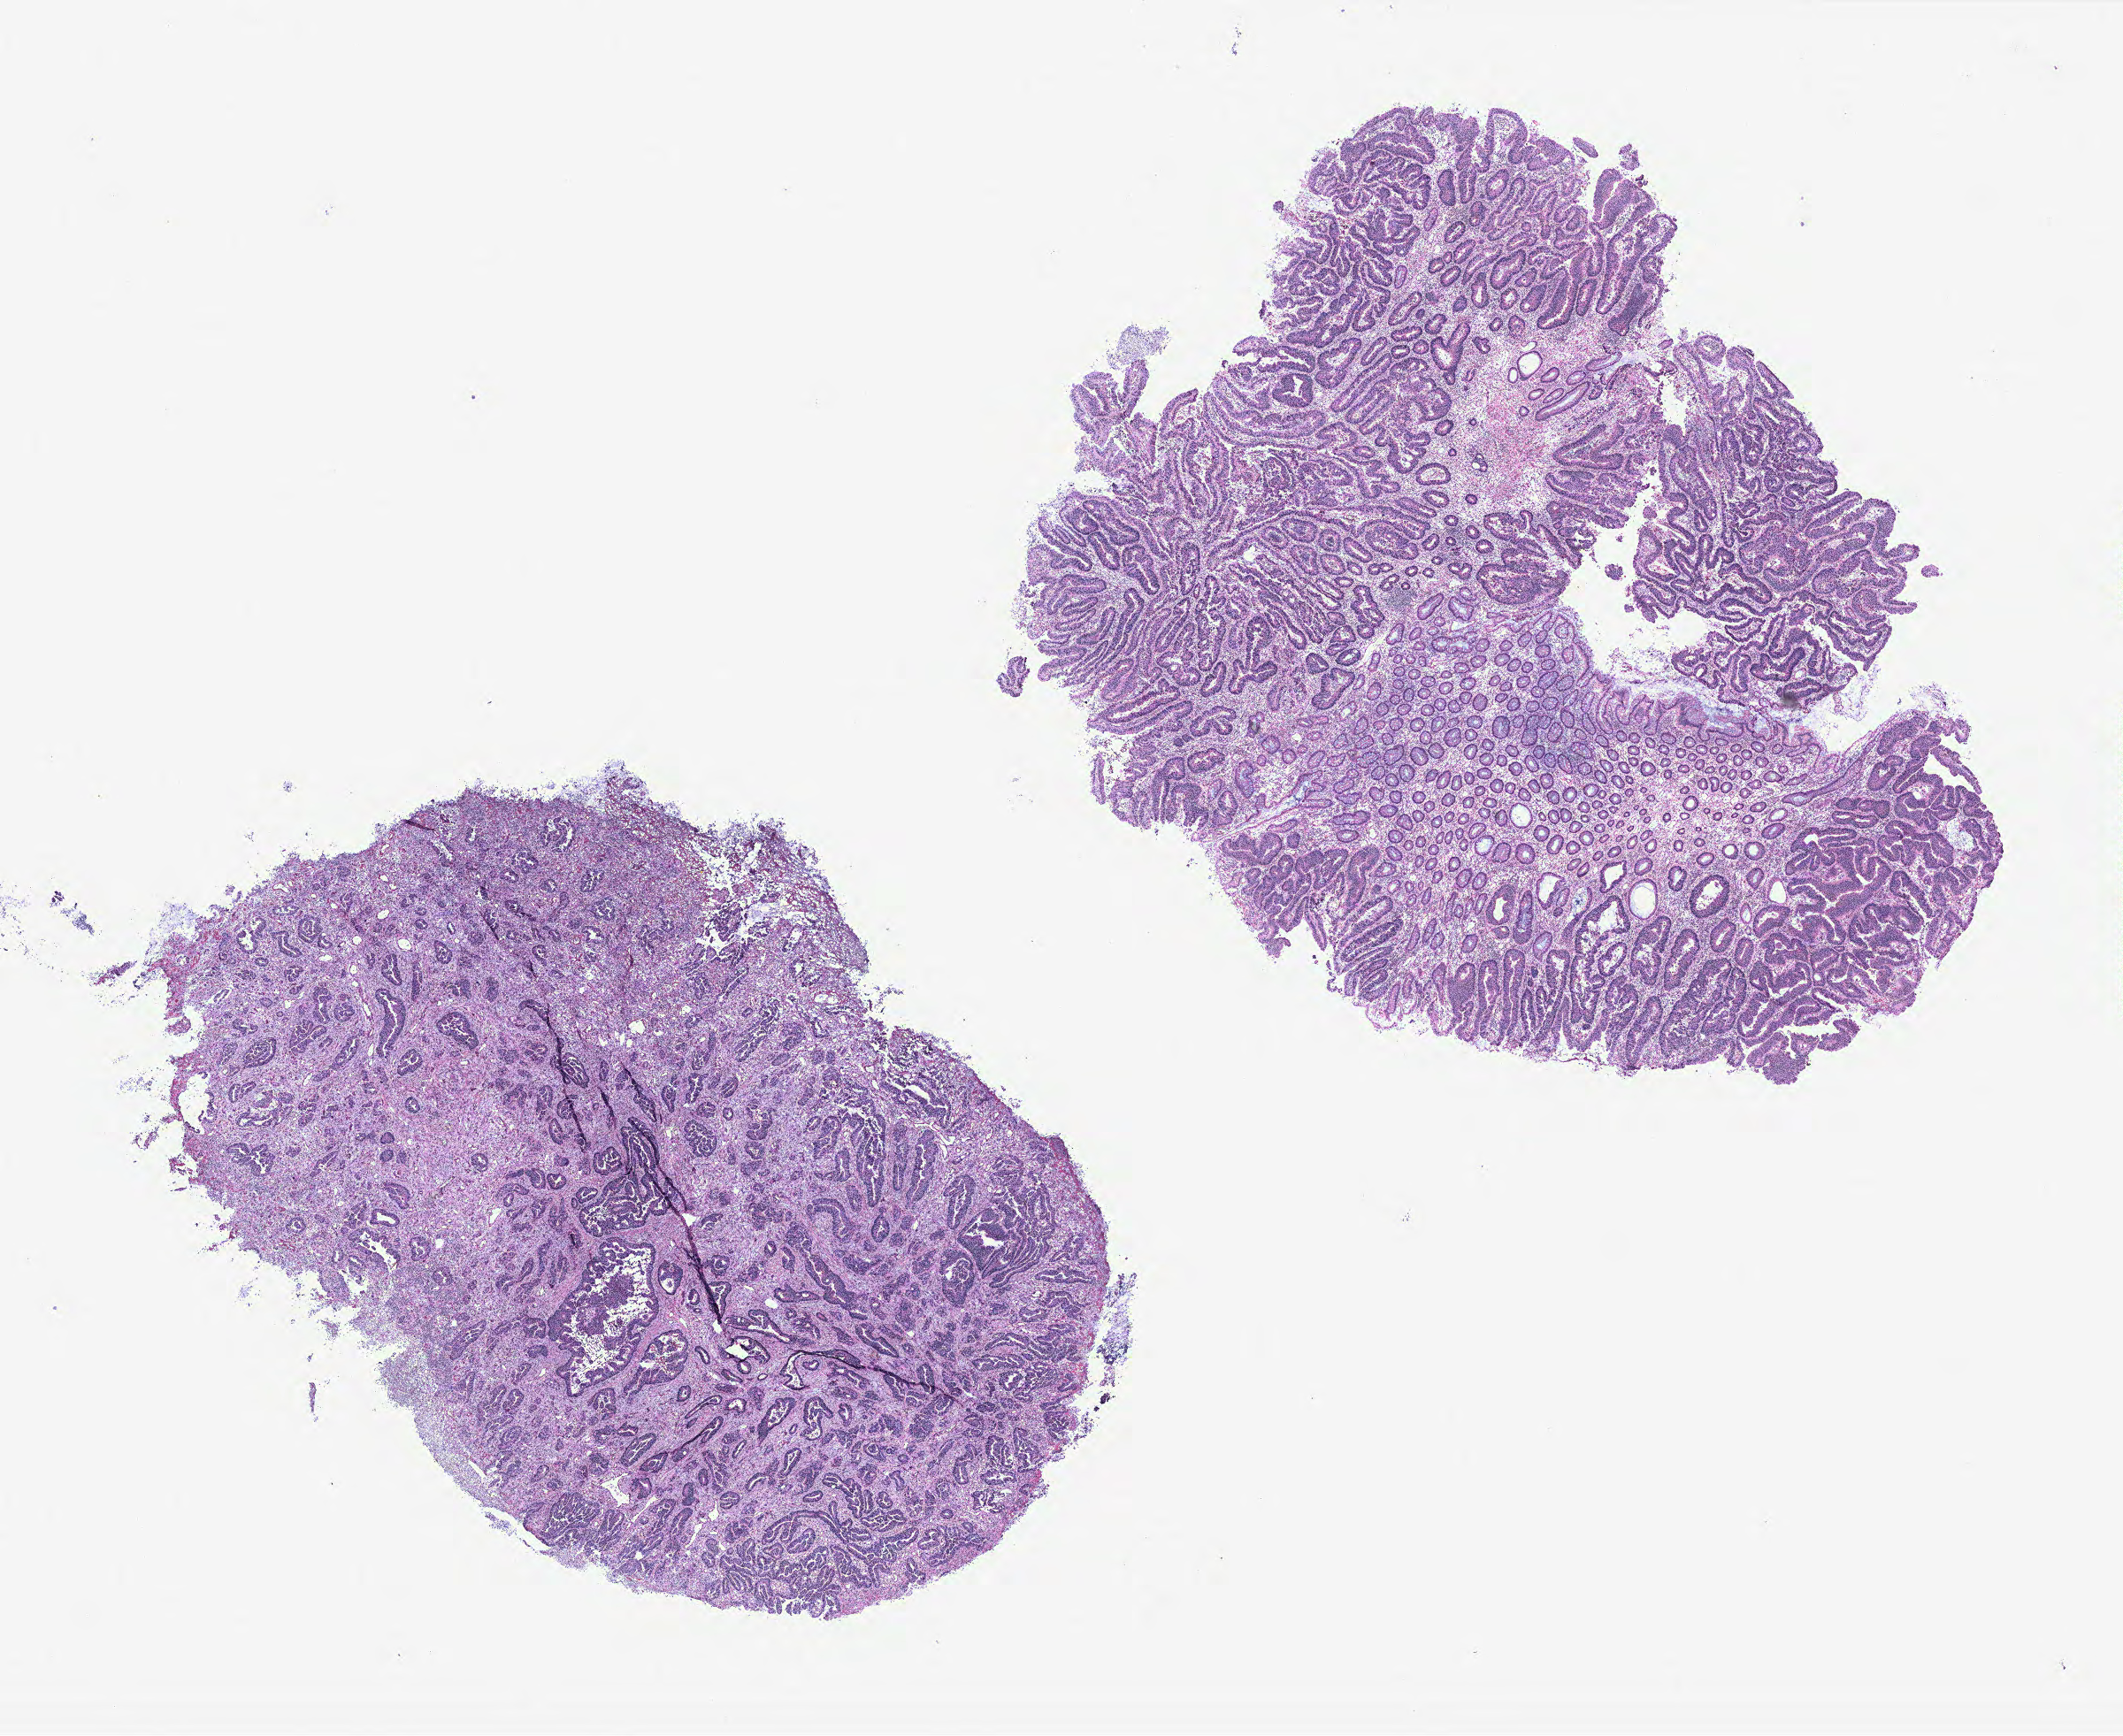
Whole-slide histology image, H&E-stained, a low-resolution overview of the entire scanned area, about 19.2 x 15.7 mm; normal (non-tumour) tissue sample, colon. 68-year-old male patient.
This section: normal (non-tumour) tissue from the same patient. Patient diagnosis: Adenocarcinoma, NOS.